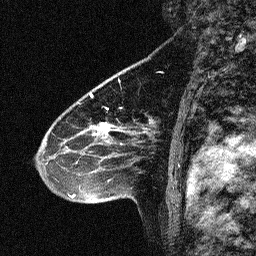
Breast MRI (dynamic contrast-enhanced), one sagittal slice. Position 42 of 64 along the scan axis. Dynamic contrast-enhanced study with each time point stored as its own series, time point 2 of 3 at this slice position (early post-contrast, ordered by acquisition time). 1.5 T. TE 4.5 ms, TR 11 ms. 256 × 256 image matrix, field of view 200 × 200 mm. Patient: female, 46 years. Case-level facts recorded for this patient, not image findings: setting: breast cancer imaged before/during neoadjuvant chemotherapy; receptor status: HER2-positive.
Annotated regions visible in this slice (semi-automatically segmented with operator editing):
- analysis volume of interest (the breast-tissue region the enhancement analysis was run in; not a lesion): bounding box (x1, y1, x2, y2) in pixels: (42, 80, 150, 180)
- tumour enhancement mask (voxels above the 90 % enhancement threshold inside the analysis volume of interest): (64, 126, 124, 164)